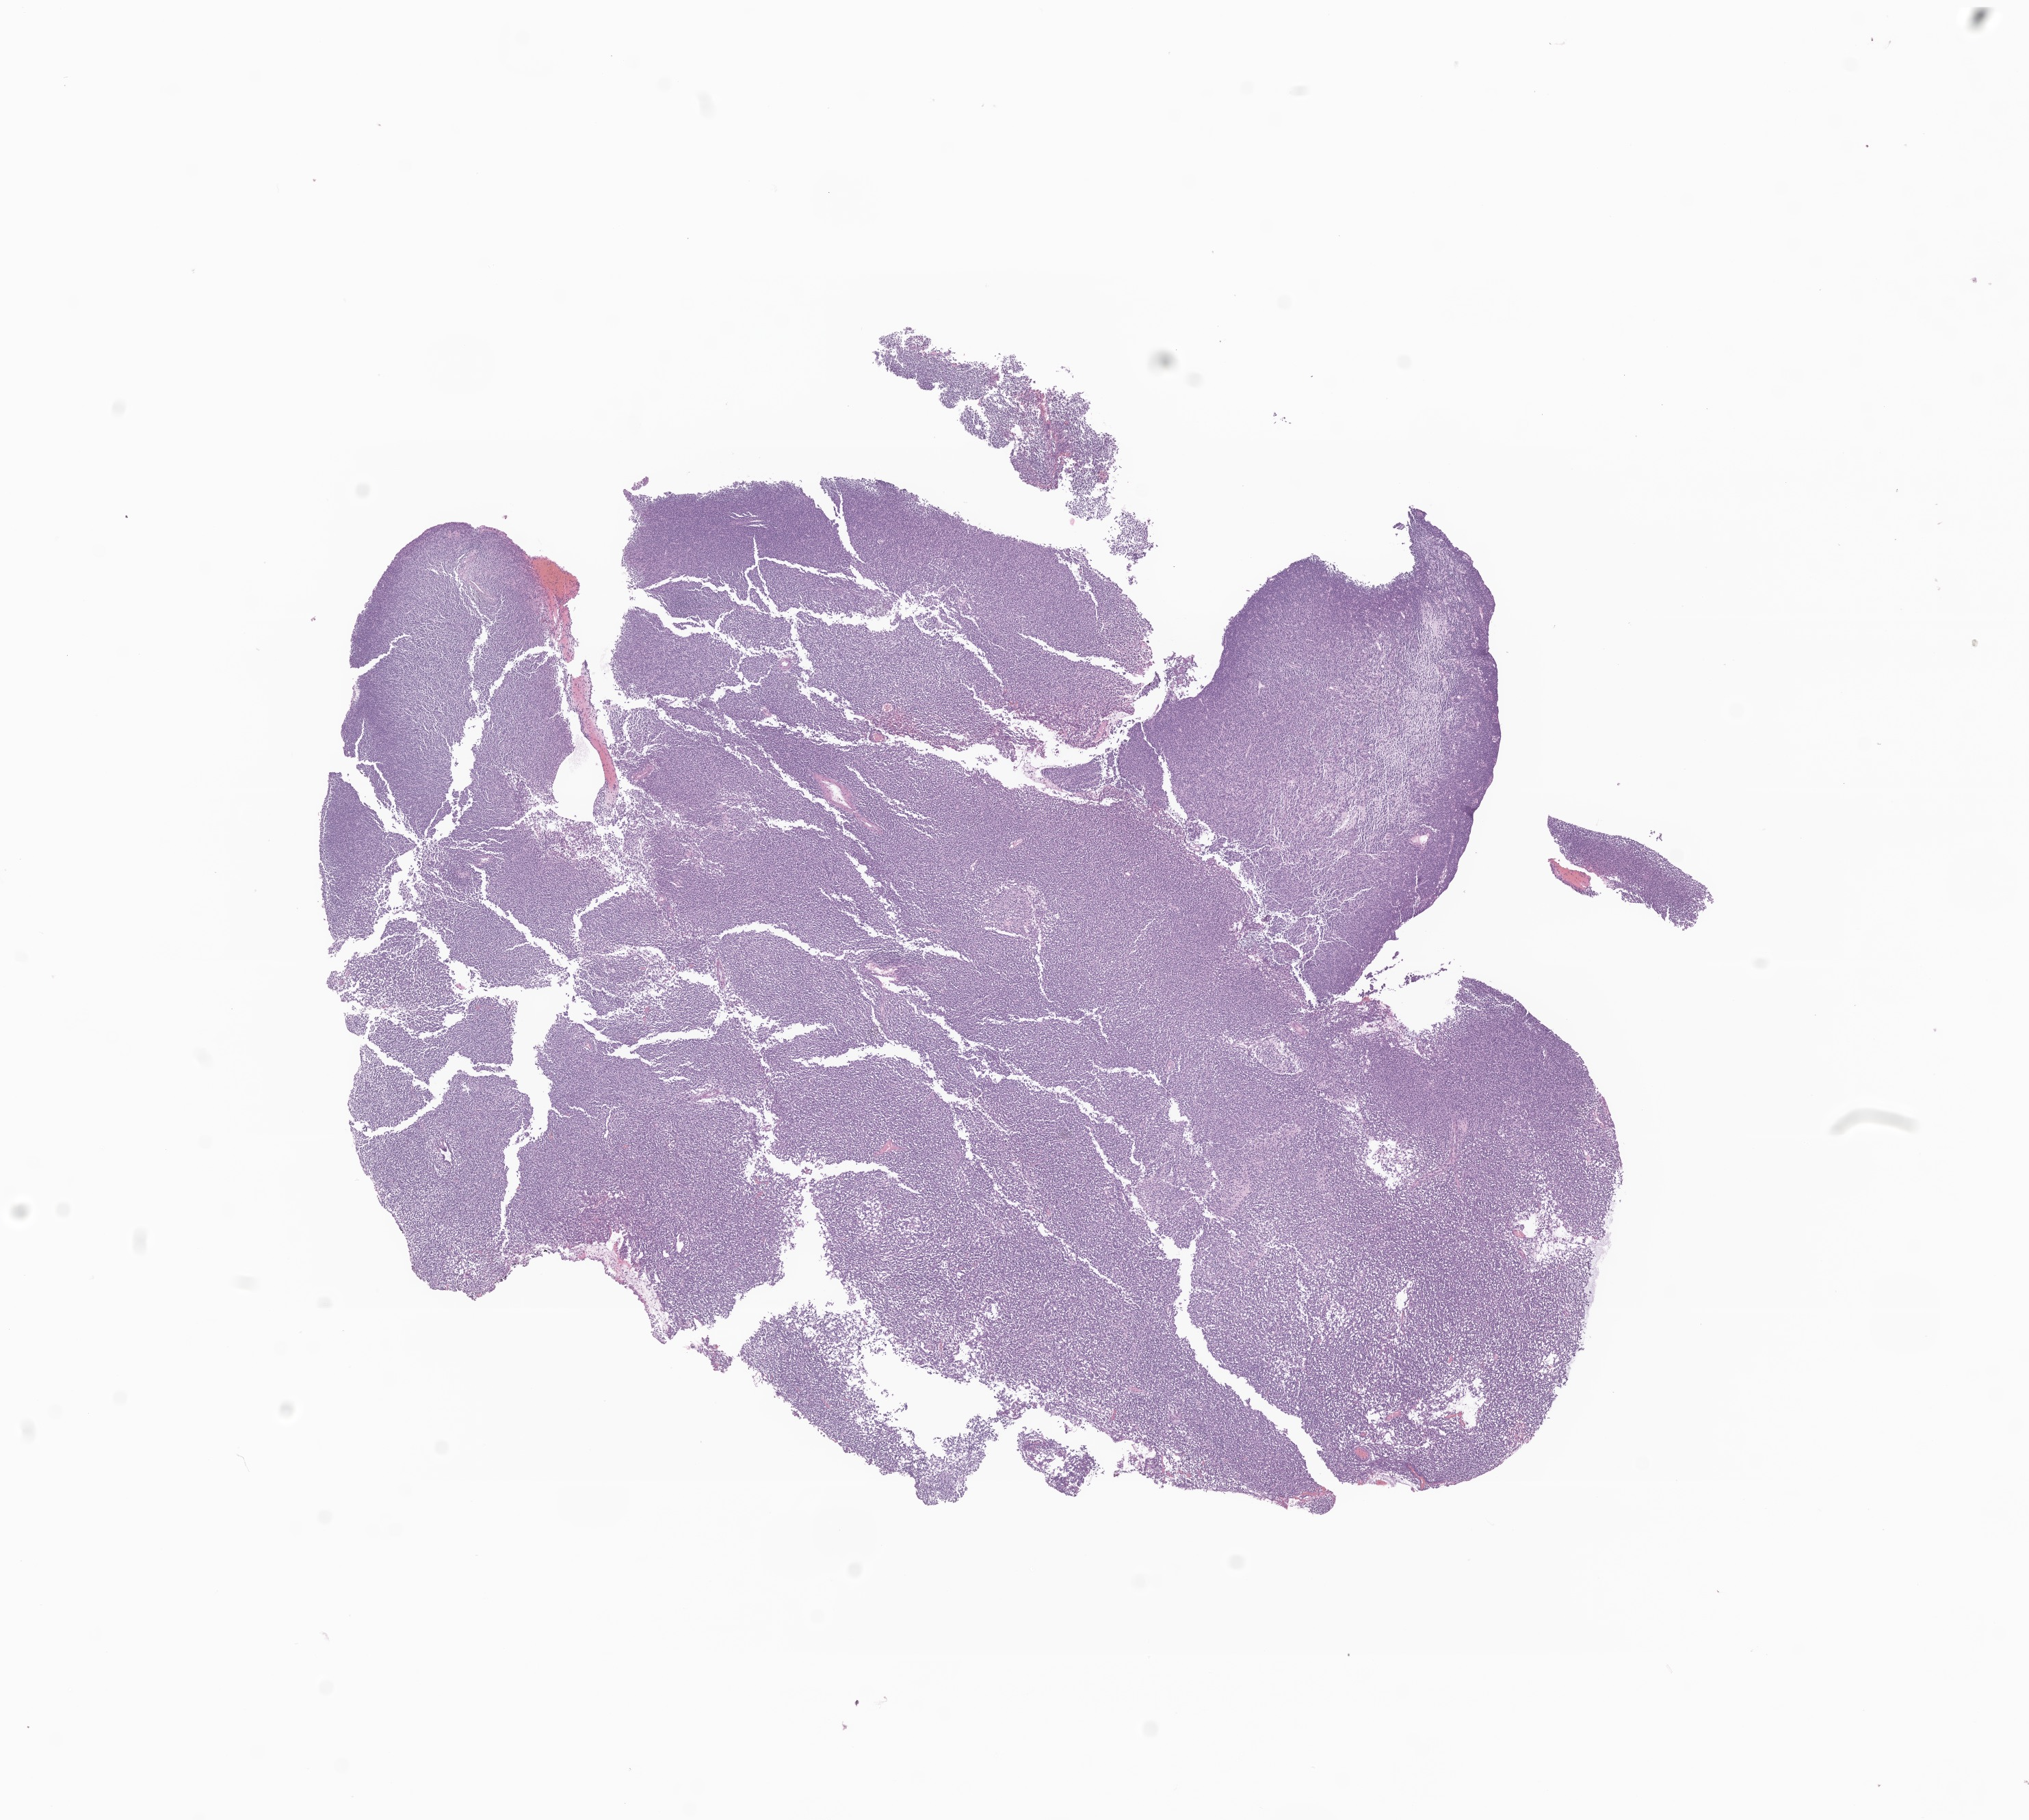
Digitized haematoxylin and eosin-stained section of tumor tissue from the brain — a low-resolution overview of the entire scanned area, about 12.5 x 11.2 mm; FFPE section. Patient male; age 274 months.
- diagnosis: Medulloblastoma, NOS